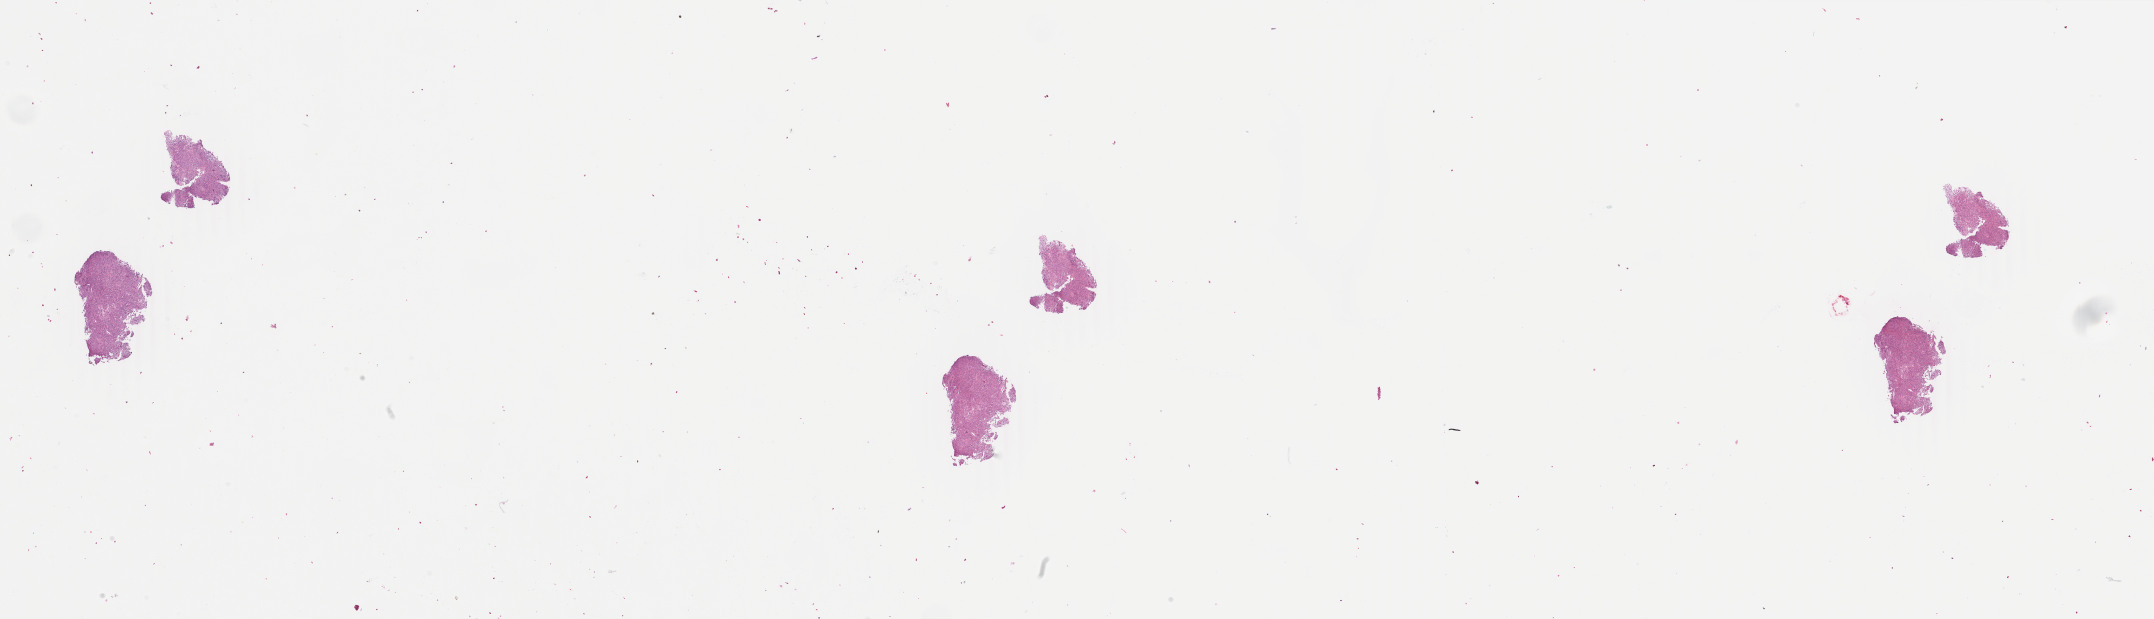
Digitized H&E-stained tissue section (whole slide), whole scanned area (about 34.3 x 9.8 mm, from a 40x scan) shown as a low-resolution overview. FFPE section. Skin, primary tumour sample. Male patient; age at initial diagnosis 62 years.
Pathologic diagnosis: Malignant melanoma, NOS.